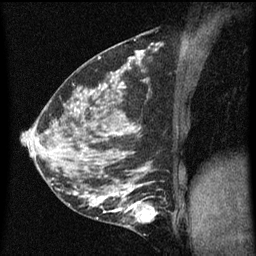
Breast MRI (dynamic contrast-enhanced), one sagittal slice; slice 27 of 60 in the series (ordered by position); dynamic contrast-enhanced series, image 2 of 5 at this slice position (ordered by acquisition); 1.5 T; TE 4.2 ms, TR 8 ms; 2 mm slice thickness; 256 × 256 image matrix, field of view 180 × 180 mm. Patient: female, 35 years.
Structures marked on this image (semi-automatic segmentation, software-assisted and operator-edited):
- analysis volume of interest (the breast-tissue region the enhancement analysis was run in; not a lesion): bounding box [x1, y1, x2, y2] px = [118, 190, 162, 229]
- tumour enhancement mask (voxels above the 70 % enhancement threshold inside the analysis volume of interest): [118, 192, 158, 221]